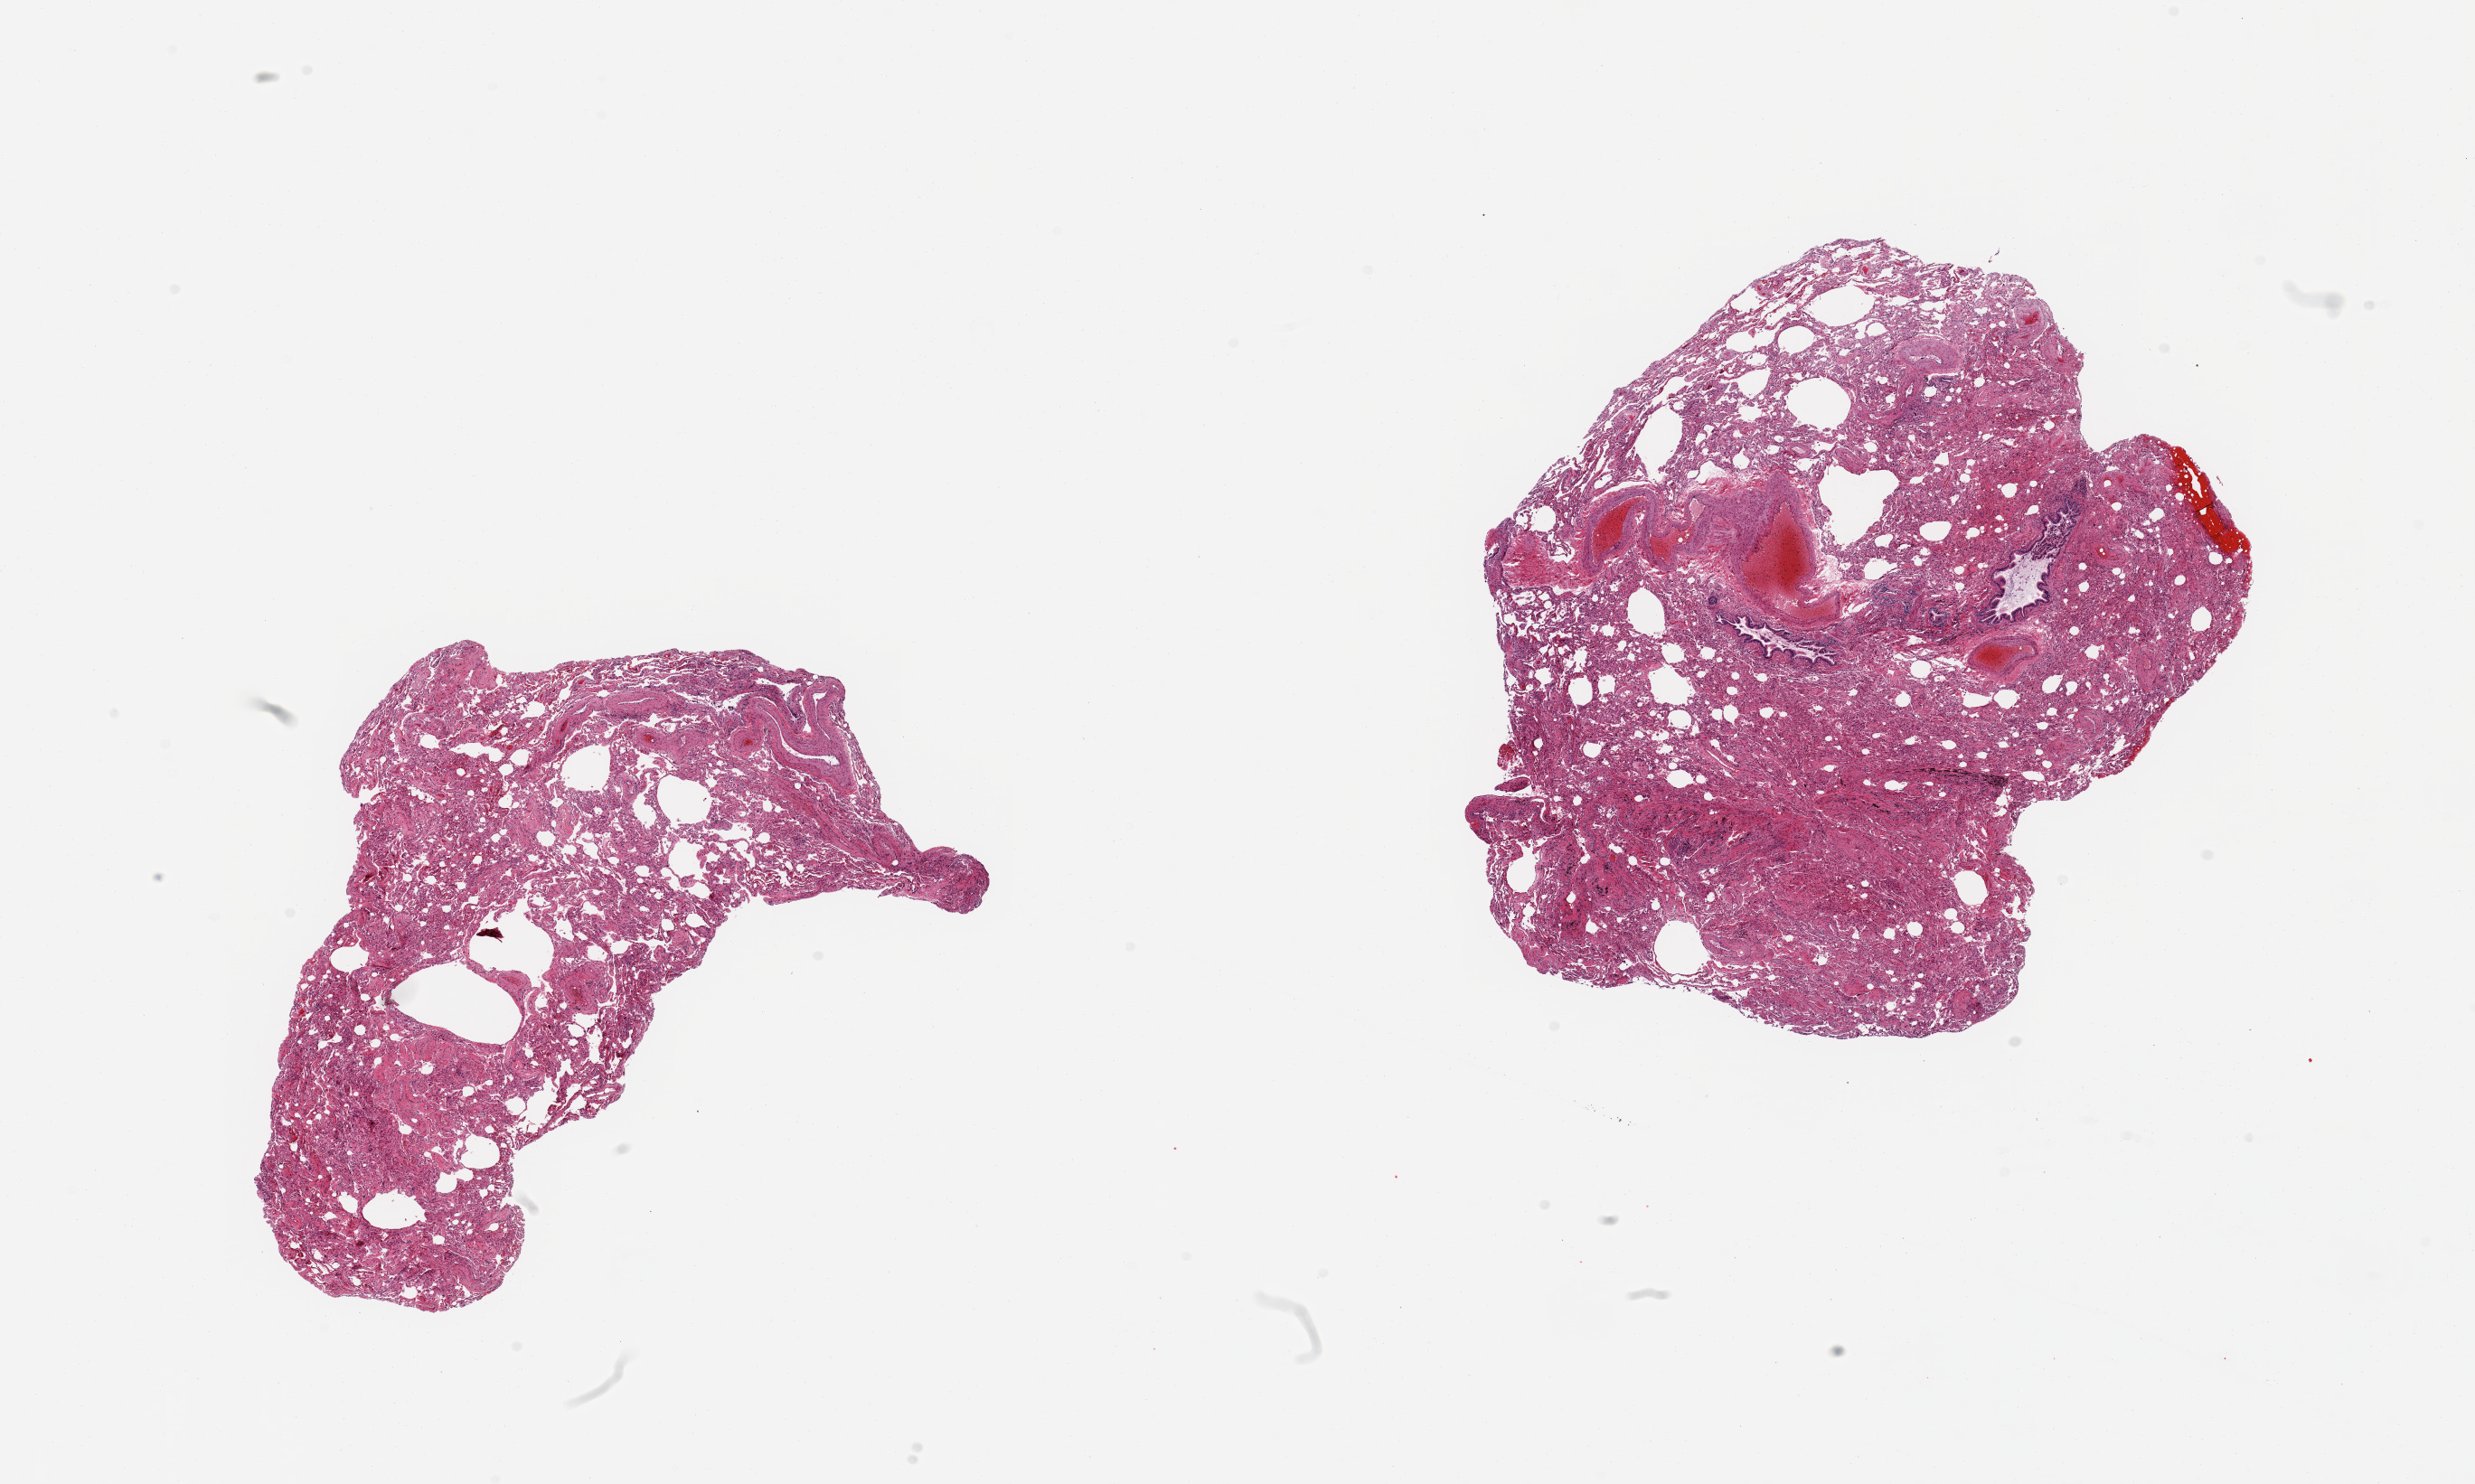
H&E whole-slide image, brightfield, a low-resolution overview of the entire scanned area, about 21.7 x 13.0 mm, PAXgene-fixed paraffin-embedded (PFPE) section, section of lung (target tissue), tissue donor sample. Donor: male.
Pathologist's review note for this sample: 2 pieces moderate congestion/atalectasis.